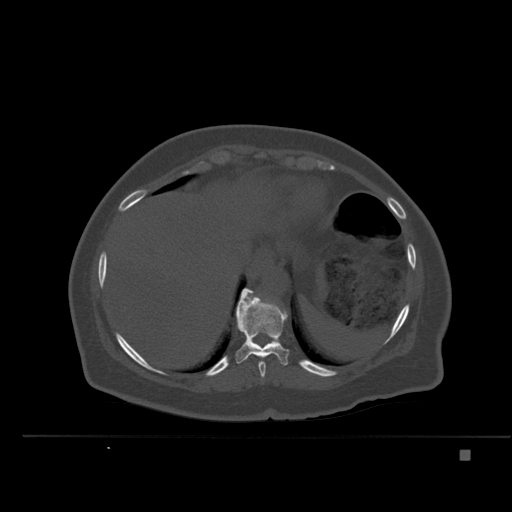
CT including the spine, one axial slice. Position 284 of 477 along the scan axis. Bone window (W 1800 / L 400 HU). 1.5 mm slice thickness. 512 × 512 image matrix. Patient: female, 74 years. From the clinical record (not read from this slice): primary cancer: colon.
Annotated regions visible in this slice (semi-automatically segmented with operator editing):
- T10 vertebra: box from (x=236, y=293) to (x=289, y=366) px
- T11 vertebra: (x=241, y=288)–(x=268, y=303)
- T9 vertebra: (x=254, y=354)–(x=270, y=378)